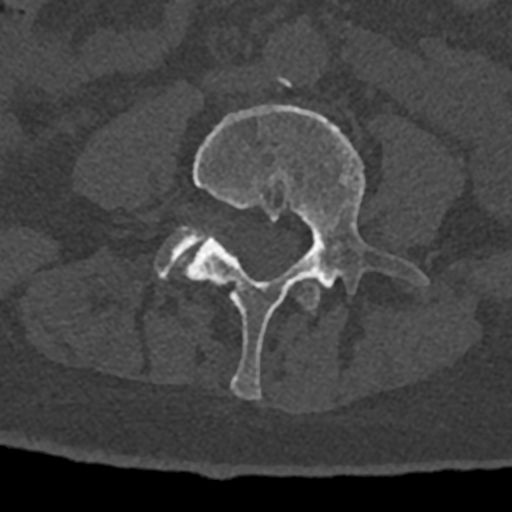
CT including the spine, one axial slice; position 256 of 797 along the scan axis; bone window (W 1800 / L 400 HU); 512 × 512 image matrix, field of view 160 × 160 mm. Patient: male, 74 years. From the clinical record (not read from this slice): primary cancer: renal.
Structures marked on this image (semi-automatic segmentation, software-assisted and operator-edited):
- L3 vertebra: bounding box <298,277,320,310> (left, top, right, bottom; pixels)
- L4 vertebra: <184,105,429,400>
- L5 vertebra: <155,226,203,279>